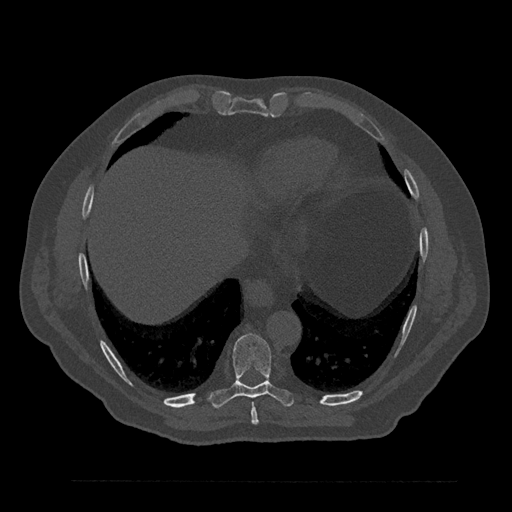
CT including the spine, one axial slice; slice 409 of 797 in the series (ordered by position); 120 kVp; bone window (W 1800 / L 400 HU); 0.5 mm slice thickness; 512 × 512 image matrix. Patient: male, 61 years. Case-level facts recorded for this patient, not image findings: primary cancer: prostate.
Annotated regions visible in this slice (semi-automatic segmentation, software-assisted and operator-edited):
- T8 vertebra: bounding box (x1, y1, x2, y2) in pixels: (251, 403, 259, 425)
- T9 vertebra: (209, 334, 294, 408)